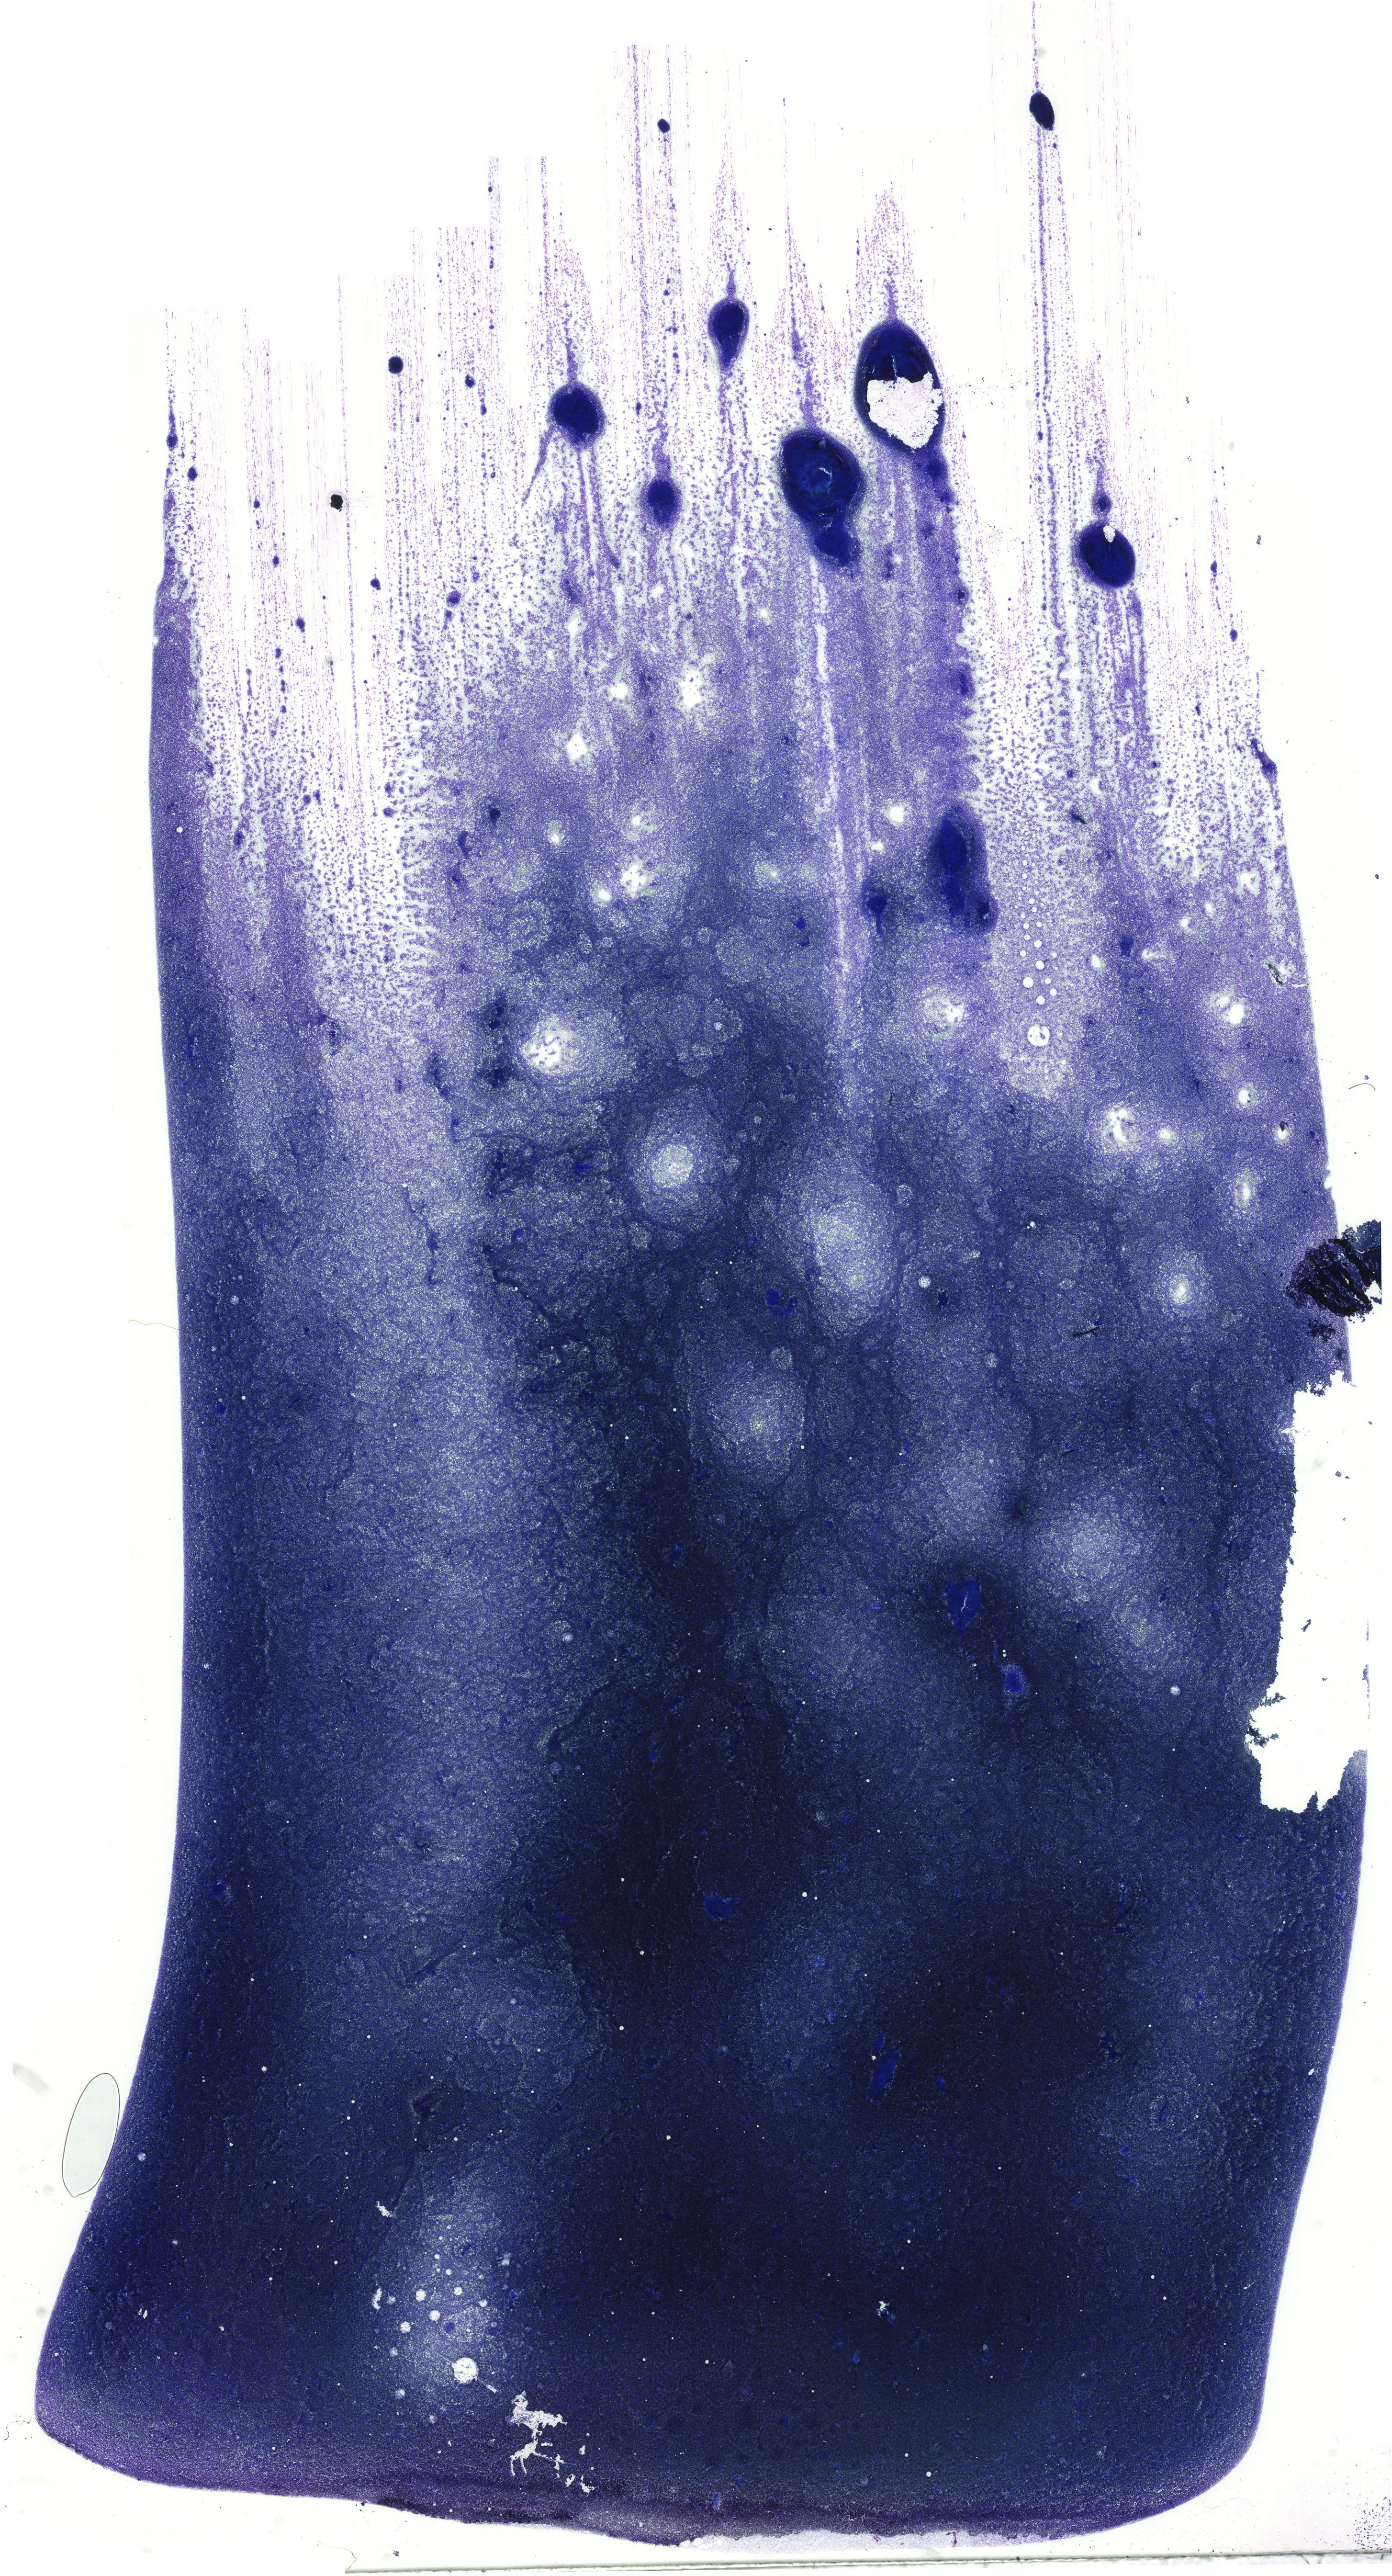
Bone marrow aspirate smear, May-Grünwald-Giemsa (MGG) stain, whole-slide image, whole scanned area (about 20.6 x 38.1 mm) shown as a low-resolution overview. Patient sex: female.
Diagnosis: Chronic Phase Chronic Myeloid Leukemia, BCR-ABL1 Positive.